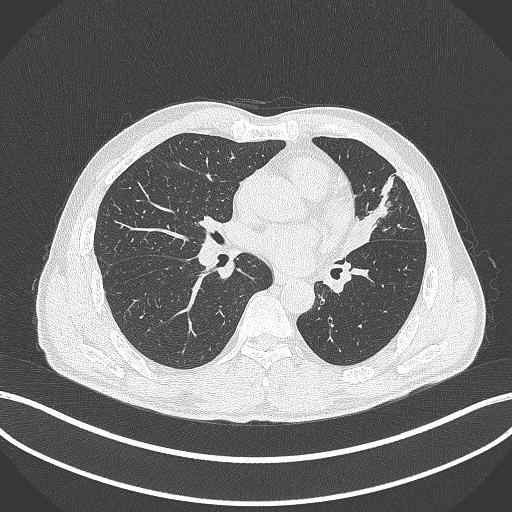
Chest CT, one axial slice; position 213 of 429 along the scan axis; reconstruction kernel B70f; lung window (W 1500 / L -600 HU); 1 mm slice thickness; 512 × 512 image matrix, field of view 400 × 400 mm. Patient: male, 57 years. From the clinical record (not read from this slice): clinical TNM (as recorded): T2b N0 M0.
Structures marked on this image (rectangle marked by the reading radiologist):
- lung tumour (recorded histology: squamous cell carcinoma): bounding box [x1, y1, x2, y2] px = [339, 204, 375, 256]